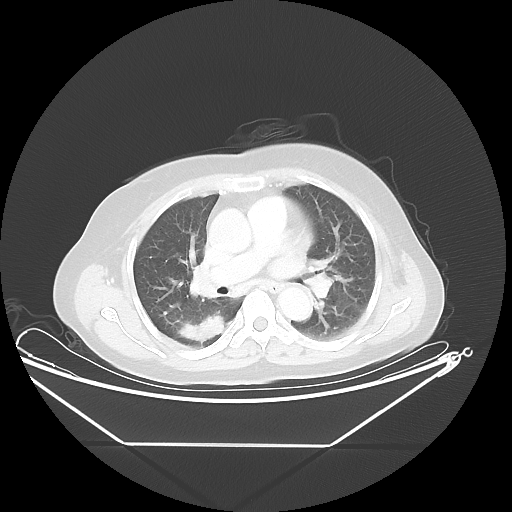
Chest CT, one axial slice; slice 27 of 48 in the series (ordered by position); reconstruction kernel LUNG; lung window (W 1500 / L -600 HU); 5 mm slice thickness; 512 × 512 image matrix, field of view 462 × 462 mm. Patient: female, 62 years. Case-level facts recorded for this patient, not image findings: clinical TNM (as recorded): T1c N0 M0; histopathological grade: G2-3.
Outlined on this slice (bounding box drawn by a radiologist):
- lung tumour (recorded histology: adenocarcinoma): bounding box (x1, y1, x2, y2) in pixels: (173, 302, 239, 356)